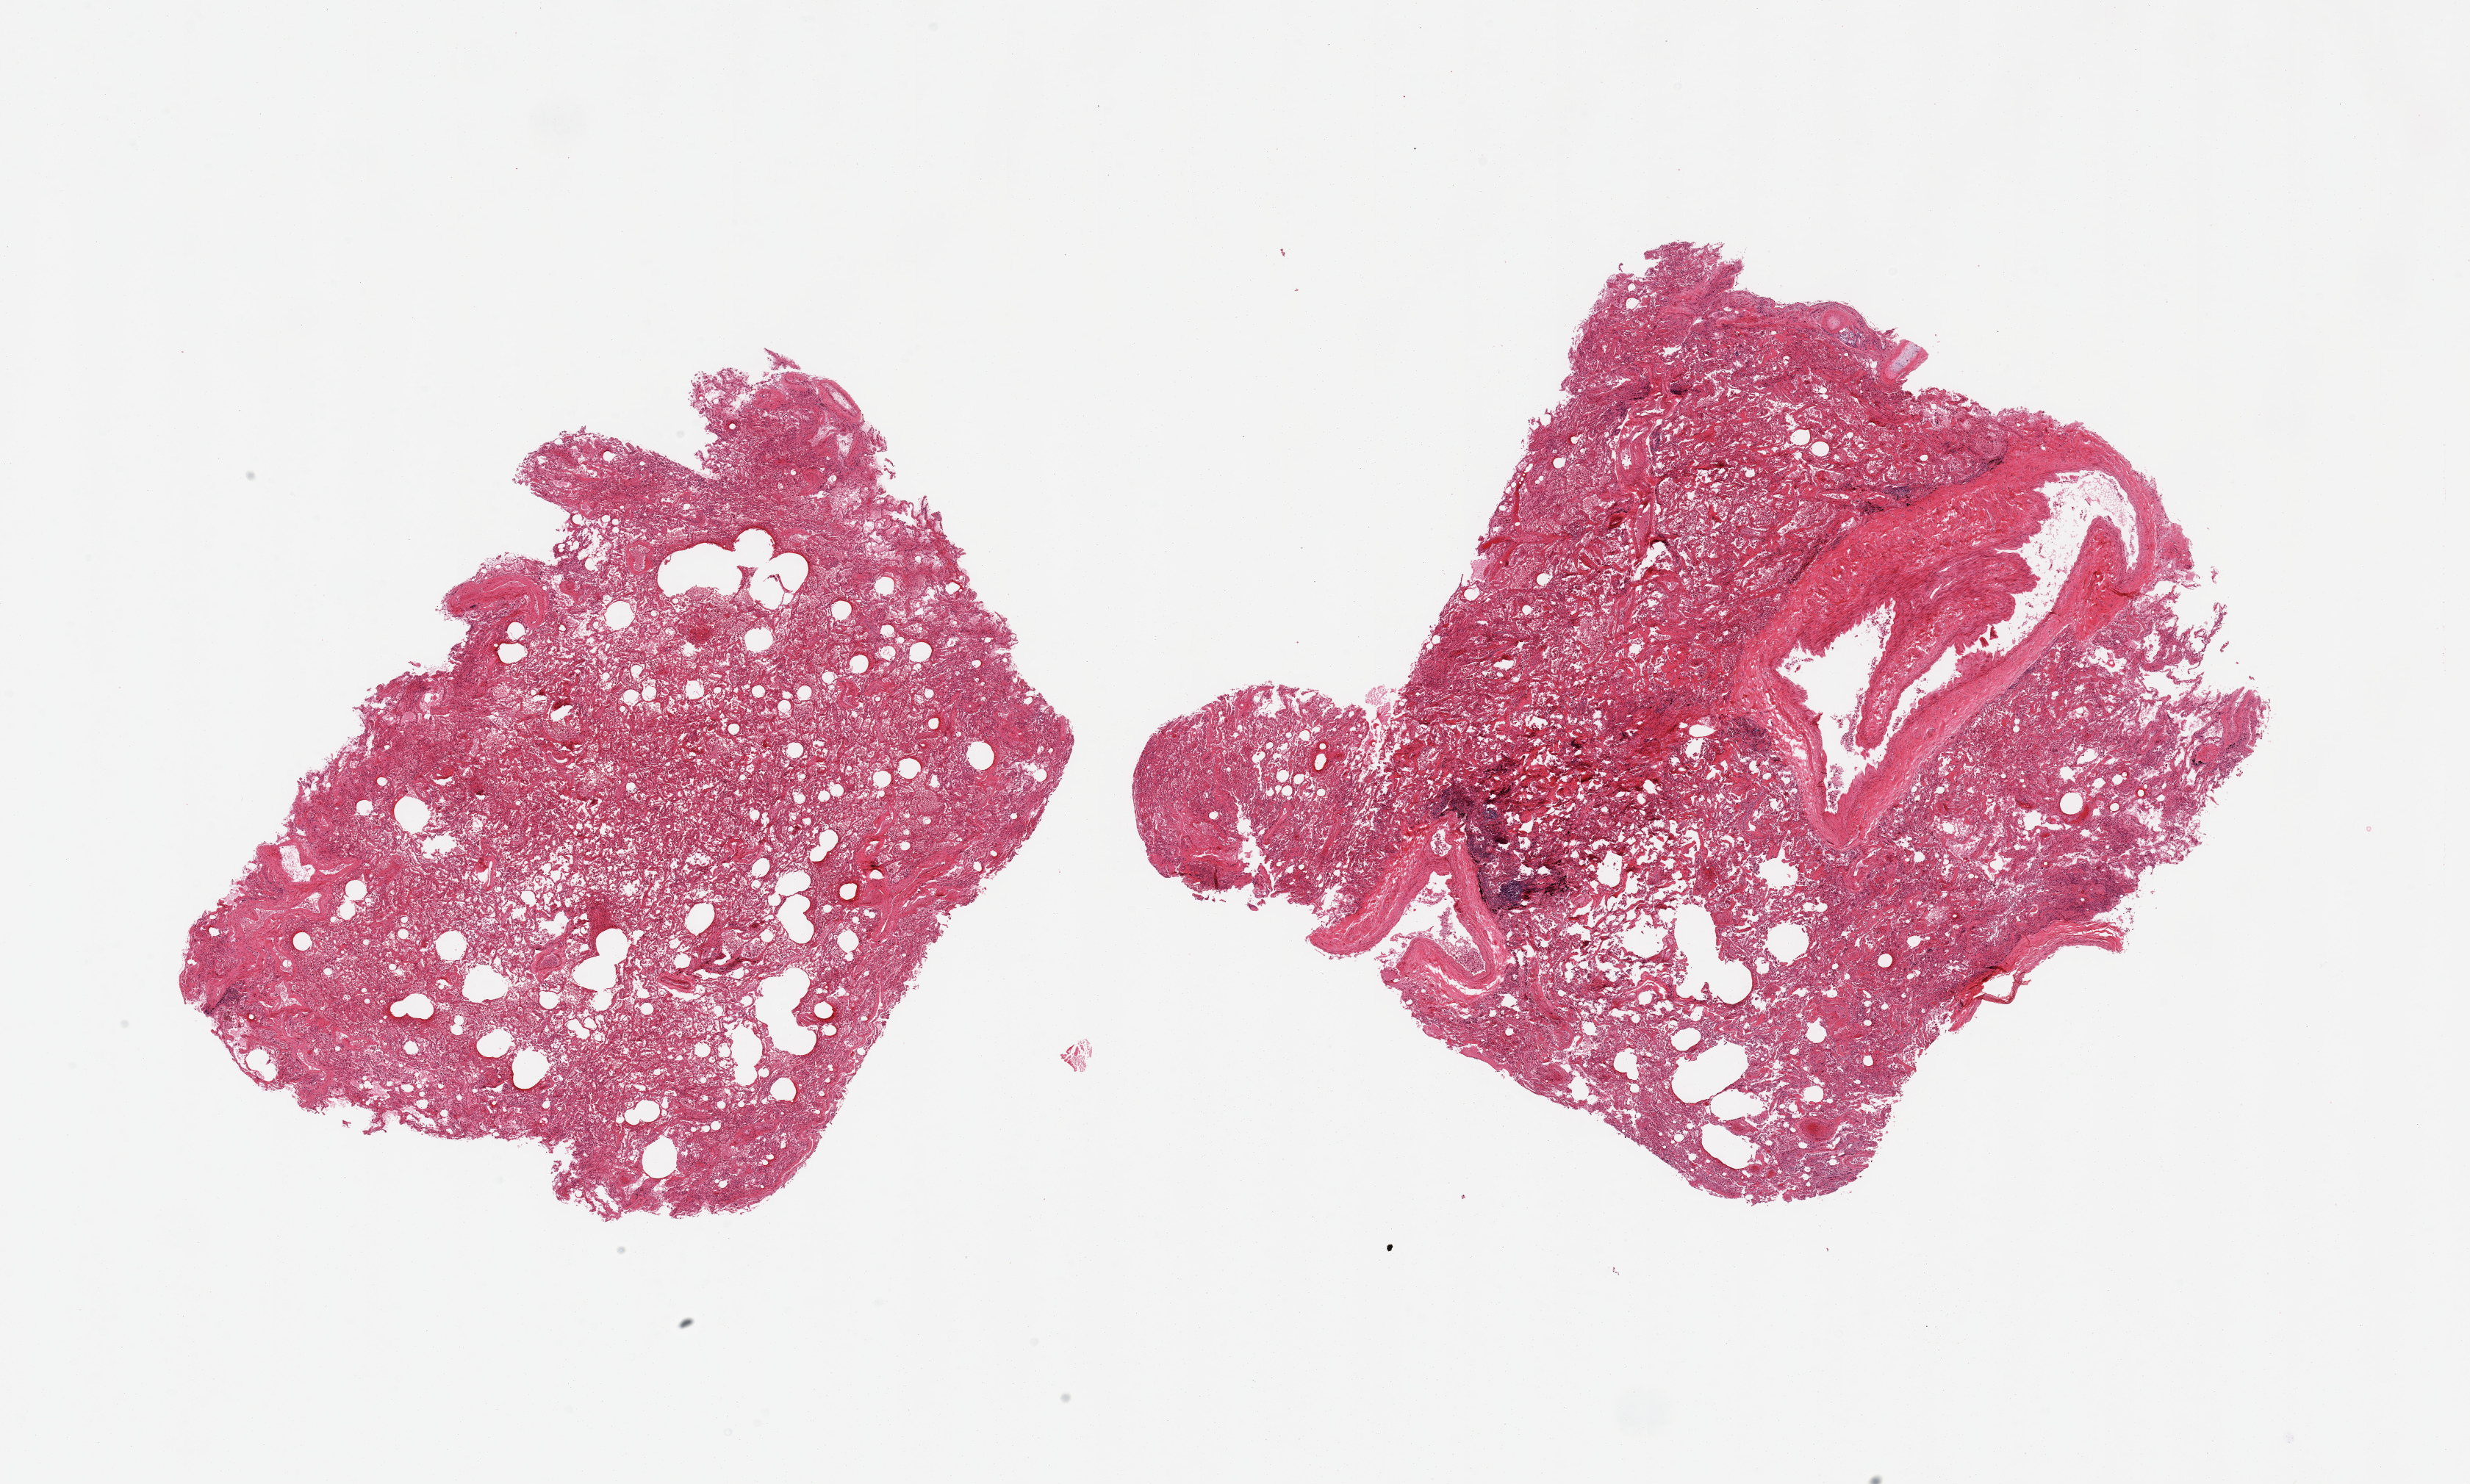
Haematoxylin and eosin whole-slide image, low-resolution overview of the scanned area, about 26.6 x 16.0 mm; PAXgene-fixed paraffin-embedded (PFPE) section; target tissue: lung; donor tissue sample. Donor sex: male.
- pathologist's review note for this sample: 2 pieces; patchy emphysema and fibrosis; pulmonary edema & congestion